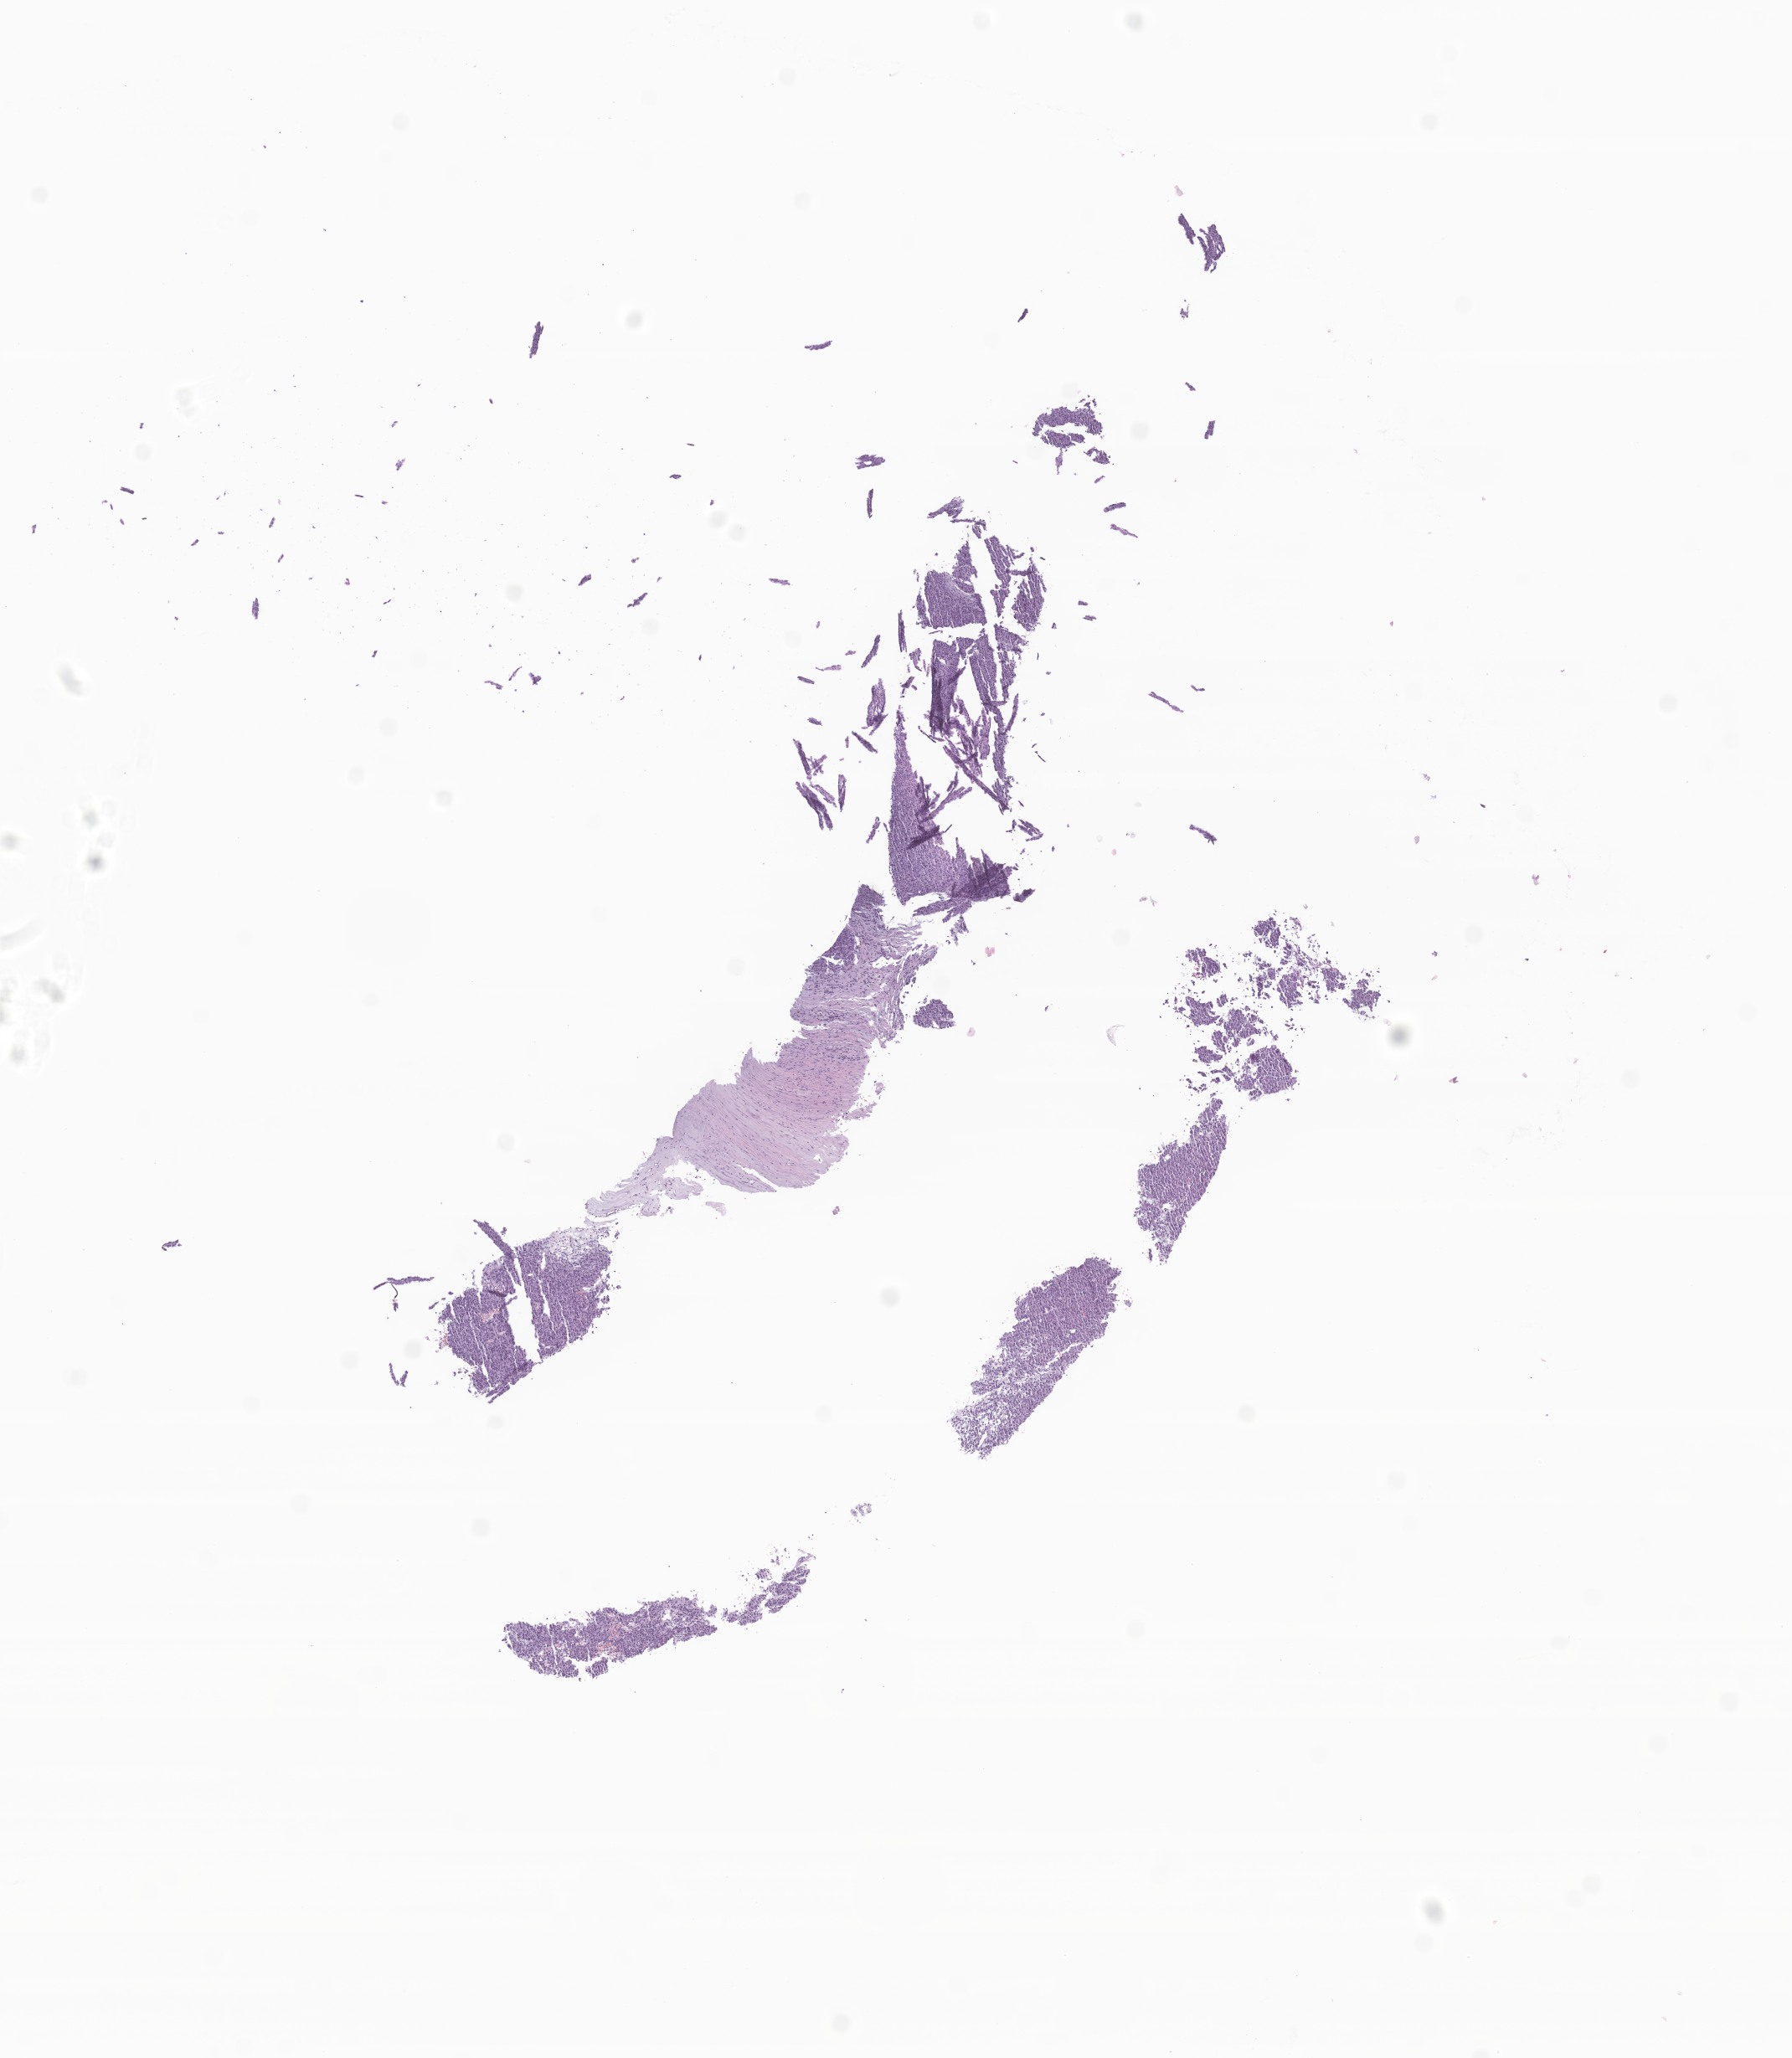
Haematoxylin and eosin whole-slide image of tumor tissue from the soft tissue of abdomen — whole scanned area (about 9.0 x 10.4 mm) shown as a low-resolution overview; formalin-fixed paraffin-embedded section. Patient male; age 223 months (18 years 7 months).
Diagnosis: Gastrointestinal stromal tumor, NOS.